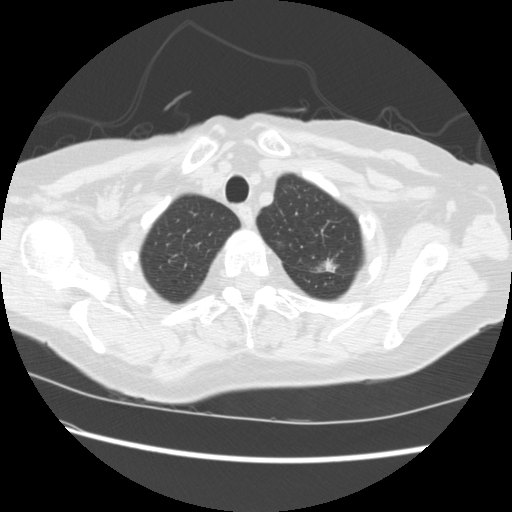
Axial slice from a low-dose chest CT screening exam. First (baseline) screen. Lung window (W 1500 / L -600 HU). Standard (soft-tissue) reconstruction kernel (STANDARD). 120 kVp. 512 × 512 image matrix, field of view 340 × 340 mm. Female, age 74 years at enrolment. Former smoker at enrolment.
Lesion marked by an expert reader, bounding box <298,249,348,285> (left, top, right, bottom; pixels). The screening reader recorded 2 non-calcified nodules or masses ≥4 mm on this exam (left upper lobe, right lower lobe); which of them this box marks is not recorded. Later outcome: lung cancer diagnosed 309 days after this screen — non-small cell carcinoma, left upper lobe, stage IV (AJCC 6th edition).